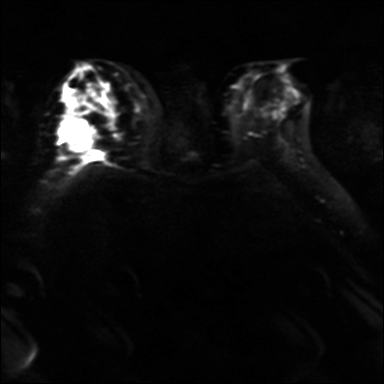
Breast MRI, one axial slice. Position 18 of 36 along the scan axis. Diffusion-weighted series; image 2 of 4 stored at this slice position (different b-values; order by instance number). 3 T. 4 mm slice thickness. 384 × 384 image matrix. Female patient.
Structures marked on this image (outlined manually by an expert reader):
- tumour on diffusion-weighted imaging: bounding box [x1, y1, x2, y2] px = [63, 119, 94, 153]